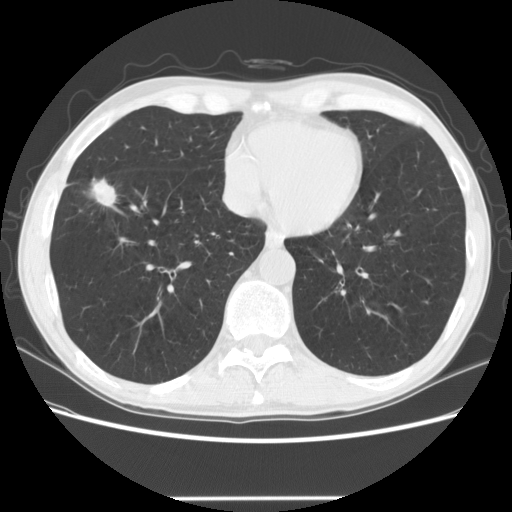
Chest CT (low-dose screening protocol), one axial image. Baseline annual screen. Lung window (W 1500 / L -600 HU). 2.5 mm slice thickness. 140 kVp. 512 × 512 image matrix. Male, age 69 years at enrolment.
• Expert-annotated lung lesion, box from (x=74, y=164) to (x=129, y=214) px.
• Screening reader's record for this exam (one nodule recorded; not confirmed to be the boxed lesion): non-calcified nodule or mass ≥4 mm, right middle lobe, 20 × 14 mm, spiculated (stellate) margins, mixed attenuation.
• Official screen result: positive, change unspecified: nodule(s) >= 4 mm or enlarging nodule(s), mass(es), or other non-specific abnormalities suspicious for lung cancer.
• Participant outcome: lung cancer diagnosed 86 days after this screen — squamous cell carcinoma, NOS, right middle lobe, poorly differentiated (G3), stage IA (AJCC 6th edition), 15 mm at pathology.